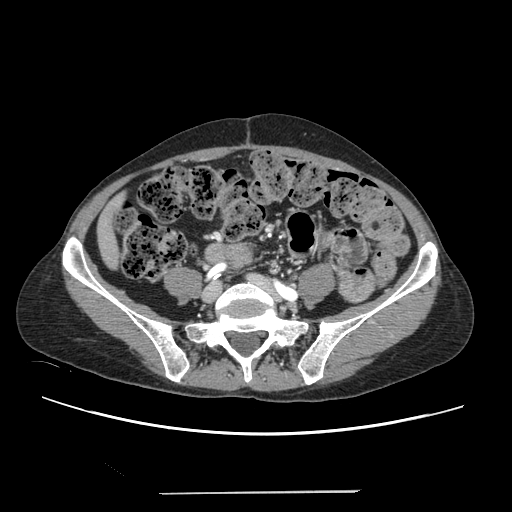
Contrast-enhanced abdominal CT, one axial slice. Slice 13 of 240 in the series (ordered by position). 120 kVp. Intravenous contrast given. Soft-tissue window (W 400 / L 40 HU). 1.25 mm slice thickness. 512 × 512 image matrix, field of view 371 × 371 mm. Female patient, age 60 years. From the clinical record (not read from this slice): diagnosis: colorectal cancer liver metastases, imaged before liver resection; multiple liver metastases: no; largest metastasis: 1.5 cm; disease in both lobes: no.
Annotated regions visible in this slice (manually delineated by an expert):
- liver: bounding box [x1, y1, x2, y2] px = [99, 209, 117, 265]
- planned liver remnant (the part of the liver to remain after resection): [99, 209, 117, 265]